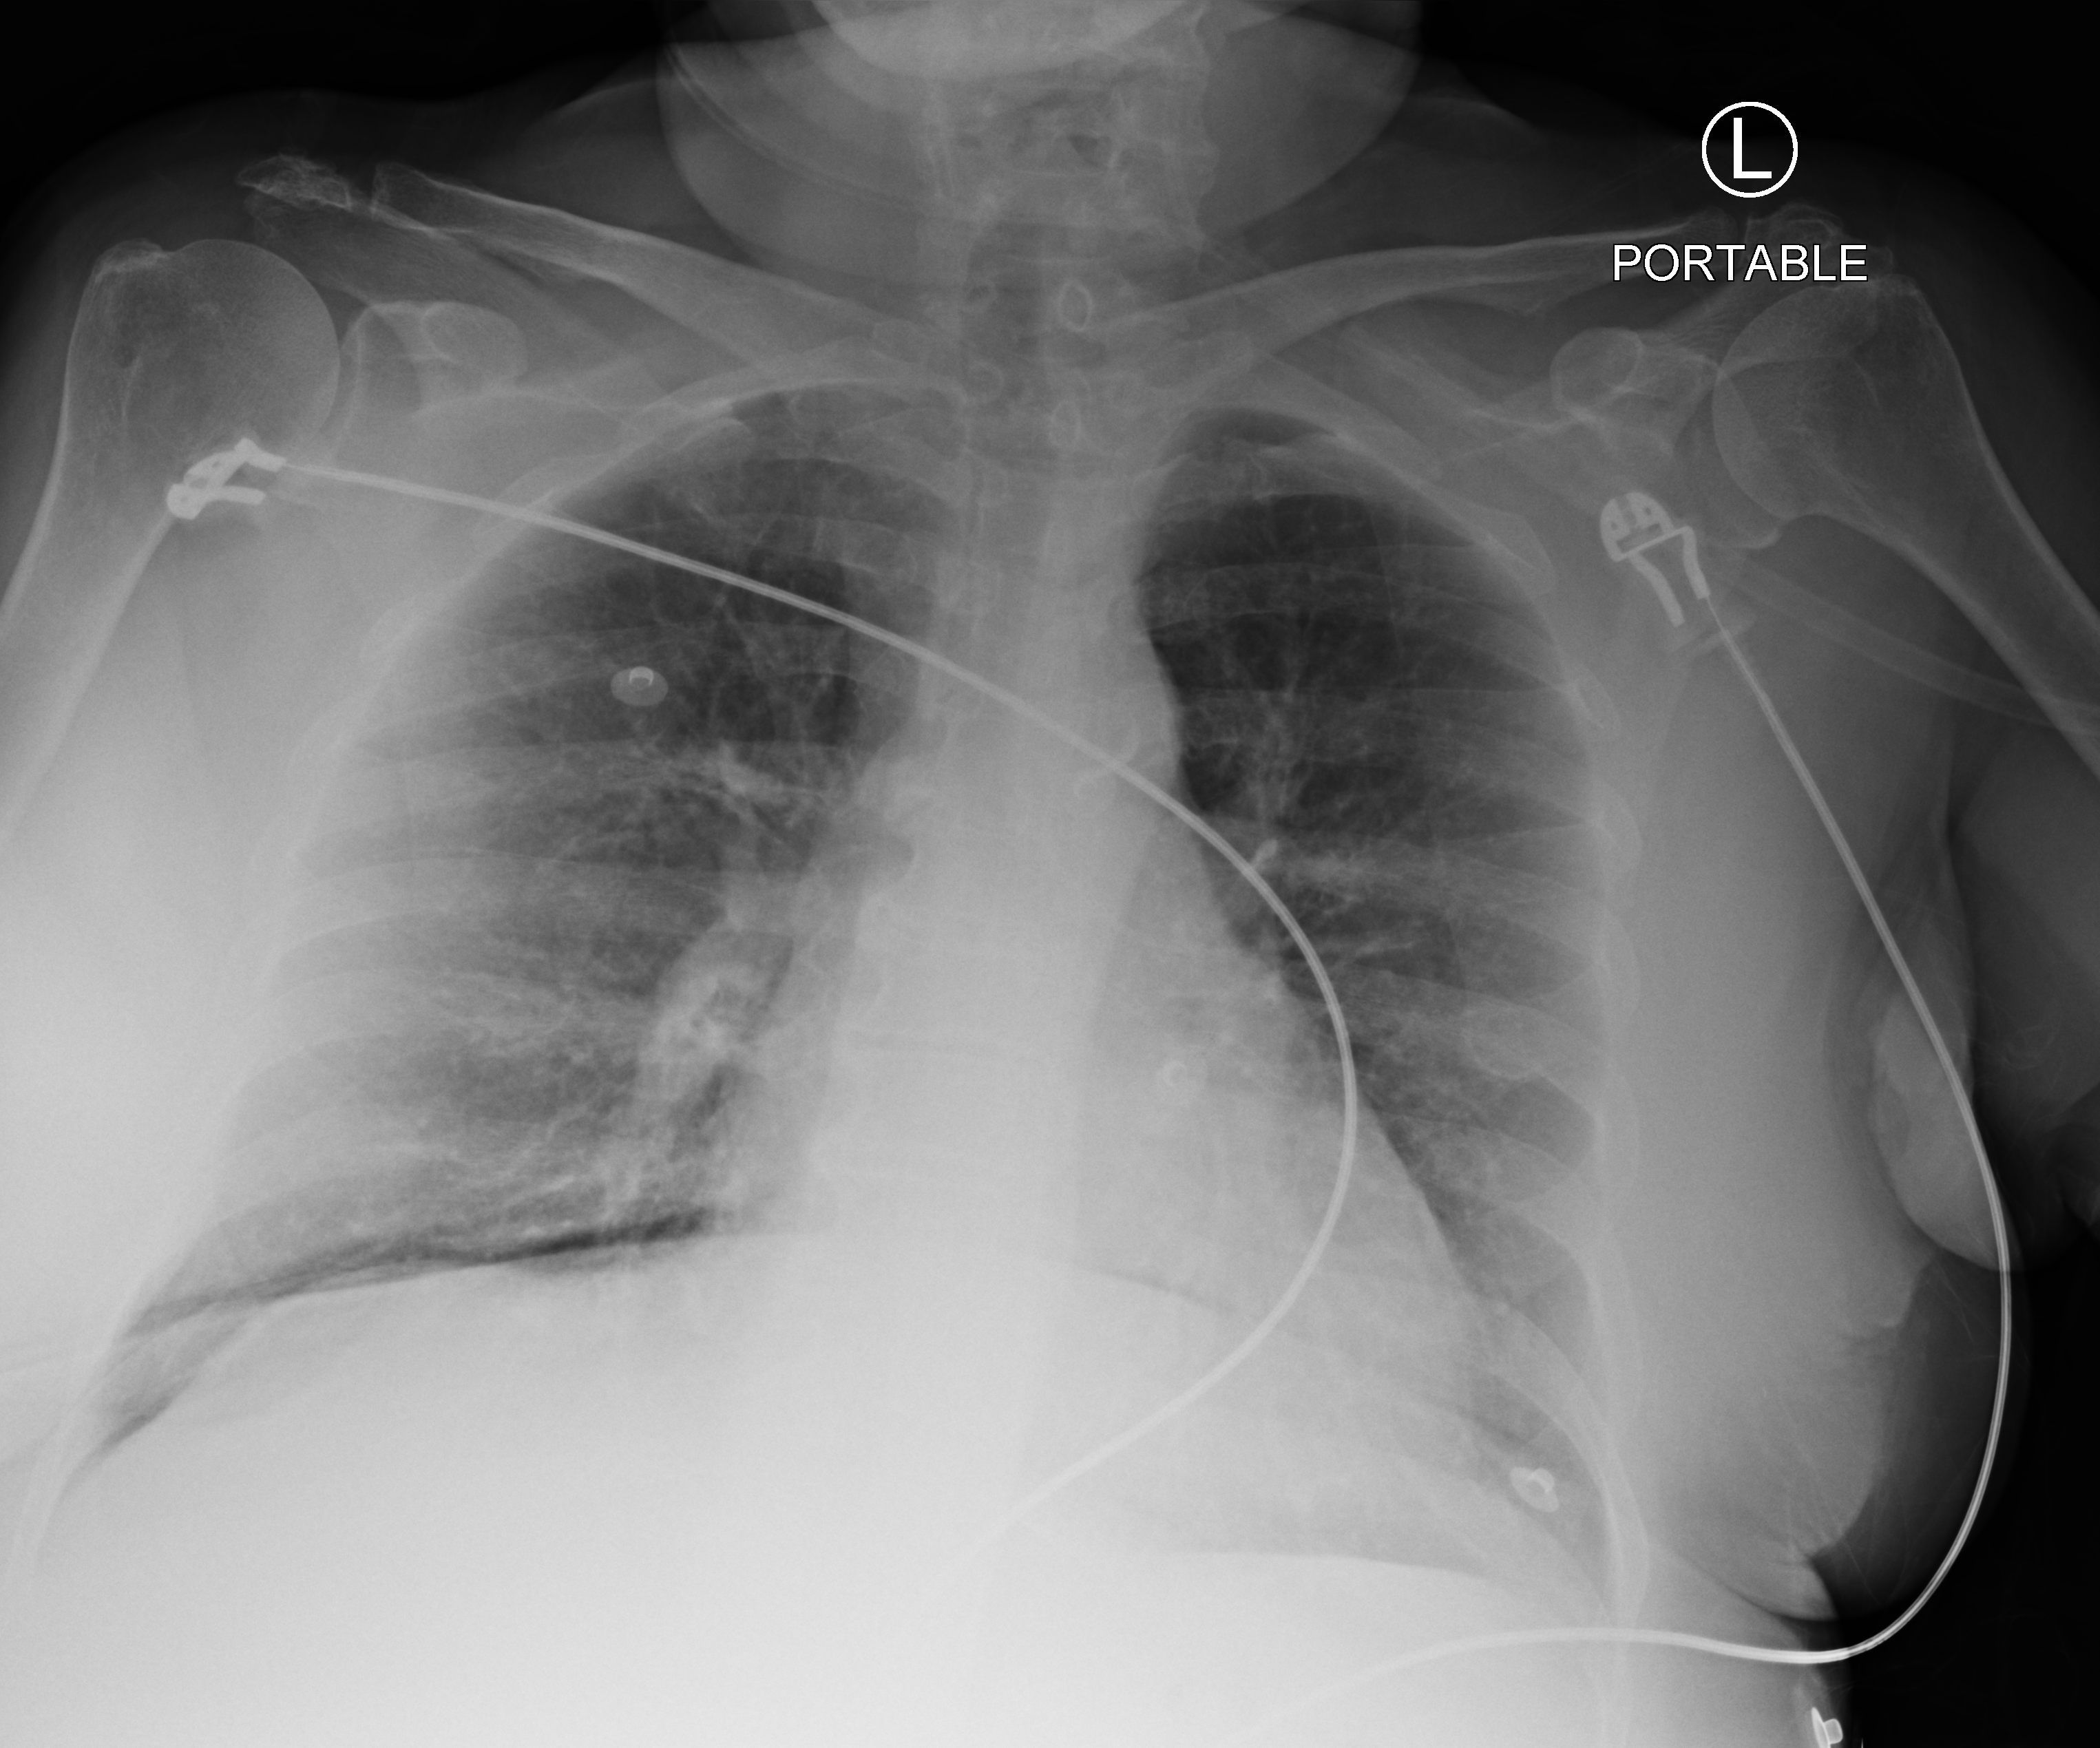
Bedside chest radiograph (computed radiography); anteroposterior (AP) projection. Female patient hospitalised with COVID-19, age 75–90 years.
From the hospital-stay record, not from the radiograph (when in the stay this image was taken is not recorded): hypertension (admission record): yes; diabetes (admission record): yes.